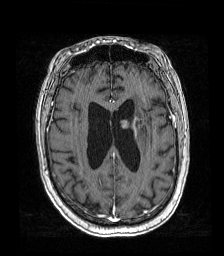
Brain MRI from a brain-tumour surgery series, one axial slice. Position 65 of 192 along the scan axis. T1-weighted post-contrast. 224 × 256 image matrix. Case-level facts recorded for this patient, not image findings: histopathology: Metastatic carcinoma from lung primary; tumour location: Left Frontal Caudate.
Outlined on this slice (expert manual segmentation):
- tumour: bounding box <117,116,148,136> (left, top, right, bottom; pixels)